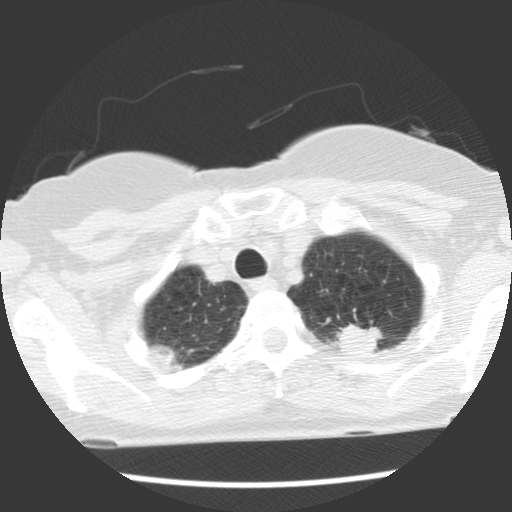
Low-dose screening chest CT, one axial slice; position 102 of 120 along the scan axis; lung window (W 1500 / L -600 HU); 2.5 mm slice thickness; 512 × 512 image matrix.
Outlined on this slice (manually delineated by an expert):
- lesion 1 (tumor, upper lobe of left lung): bounding box (x1, y1, x2, y2) in pixels: (332, 324, 383, 355)